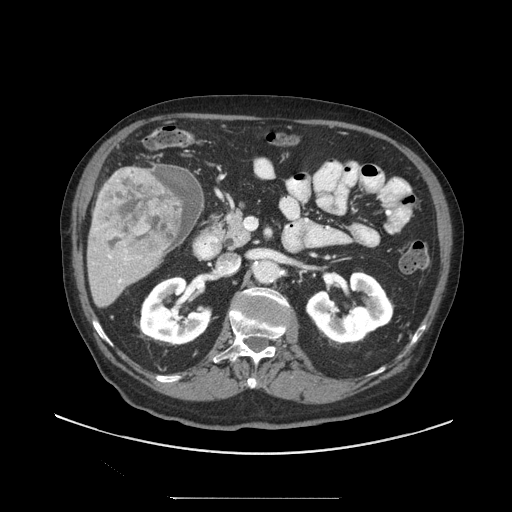
Contrast-enhanced abdominal CT (liver protocol), one axial slice. Position 42 of 97 along the scan axis. Reconstruction kernel STANDARD. 140 kVp. Soft-tissue window (W 400 / L 40 HU). 512 × 512 image matrix, field of view 450 × 450 mm. From the clinical record (not read from this slice): diagnosis: hepatocellular carcinoma (patient treated with transarterial chemoembolisation; whether this scan precedes or follows treatment is not stated here); TNM stage (as recorded): Stage-IIIC; Child-Pugh class: A; tumour differentiation: well differentiated; tumour nodularity: uninodular.
Structures marked on this image (semi-automatically segmented with operator editing):
- liver parenchyma outside the tumour (the mass and vessels are separate outlines, so this box may not span the whole liver): bounding box (x1, y1, x2, y2) in pixels: (86, 166, 182, 308)
- mass: (97, 168, 183, 257)
- liver vessels: (96, 228, 126, 282)